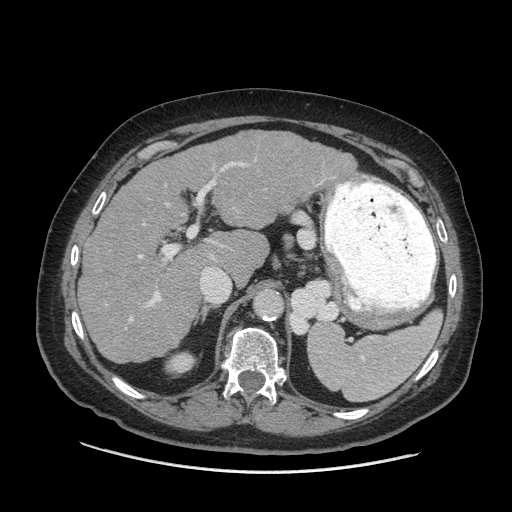
Contrast-enhanced abdominal CT (liver protocol), one axial slice; position 41 of 77 along the scan axis; reconstruction kernel STANDARD; soft-tissue window (W 400 / L 40 HU); 2.5 mm slice thickness; 512 × 512 image matrix, field of view 420 × 420 mm. Case-level facts recorded for this patient, not image findings: diagnosis: hepatocellular carcinoma (patient treated with transarterial chemoembolisation; whether this scan precedes or follows treatment is not stated here); TNM stage (as recorded): Stage-I; Child-Pugh class: A; tumour nodularity: uninodular; tumour size: 3.8 cm.
Annotated regions visible in this slice (semi-automatic segmentation, software-assisted and operator-edited):
- liver parenchyma outside the tumour (the mass and vessels are separate outlines, so this box may not span the whole liver): bounding box <78,130,356,362> (left, top, right, bottom; pixels)
- liver vessels: <129,162,323,322>